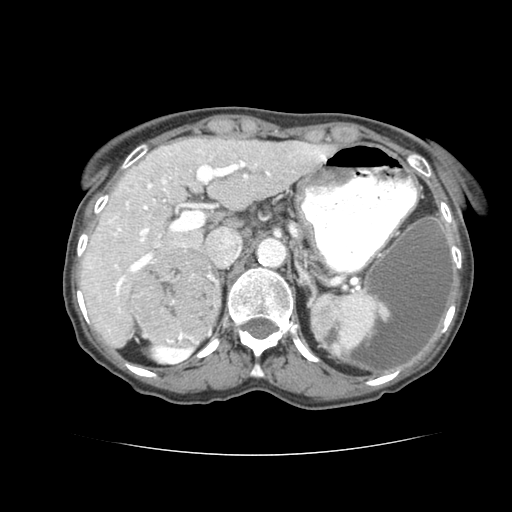
Contrast-enhanced abdominal CT (liver protocol), one axial slice. Slice 49 of 77 in the series (ordered by position). Reconstruction kernel STANDARD. Soft-tissue window (W 400 / L 40 HU). 2.5 mm slice thickness. 512 × 512 image matrix. Case-level facts recorded for this patient, not image findings: diagnosis: hepatocellular carcinoma (patient treated with transarterial chemoembolisation; whether this scan precedes or follows treatment is not stated here); TNM stage (as recorded): Stage-I; Child-Pugh class: A; tumour differentiation: well differentiated; tumour nodularity: uninodular.
Structures marked on this image (semi-automatically segmented with operator editing):
- liver parenchyma outside the tumour (the mass and vessels are separate outlines, so this box may not span the whole liver): bounding box [x1, y1, x2, y2] px = [80, 133, 356, 347]
- mass: [130, 249, 220, 347]
- liver vessels: [86, 148, 266, 319]